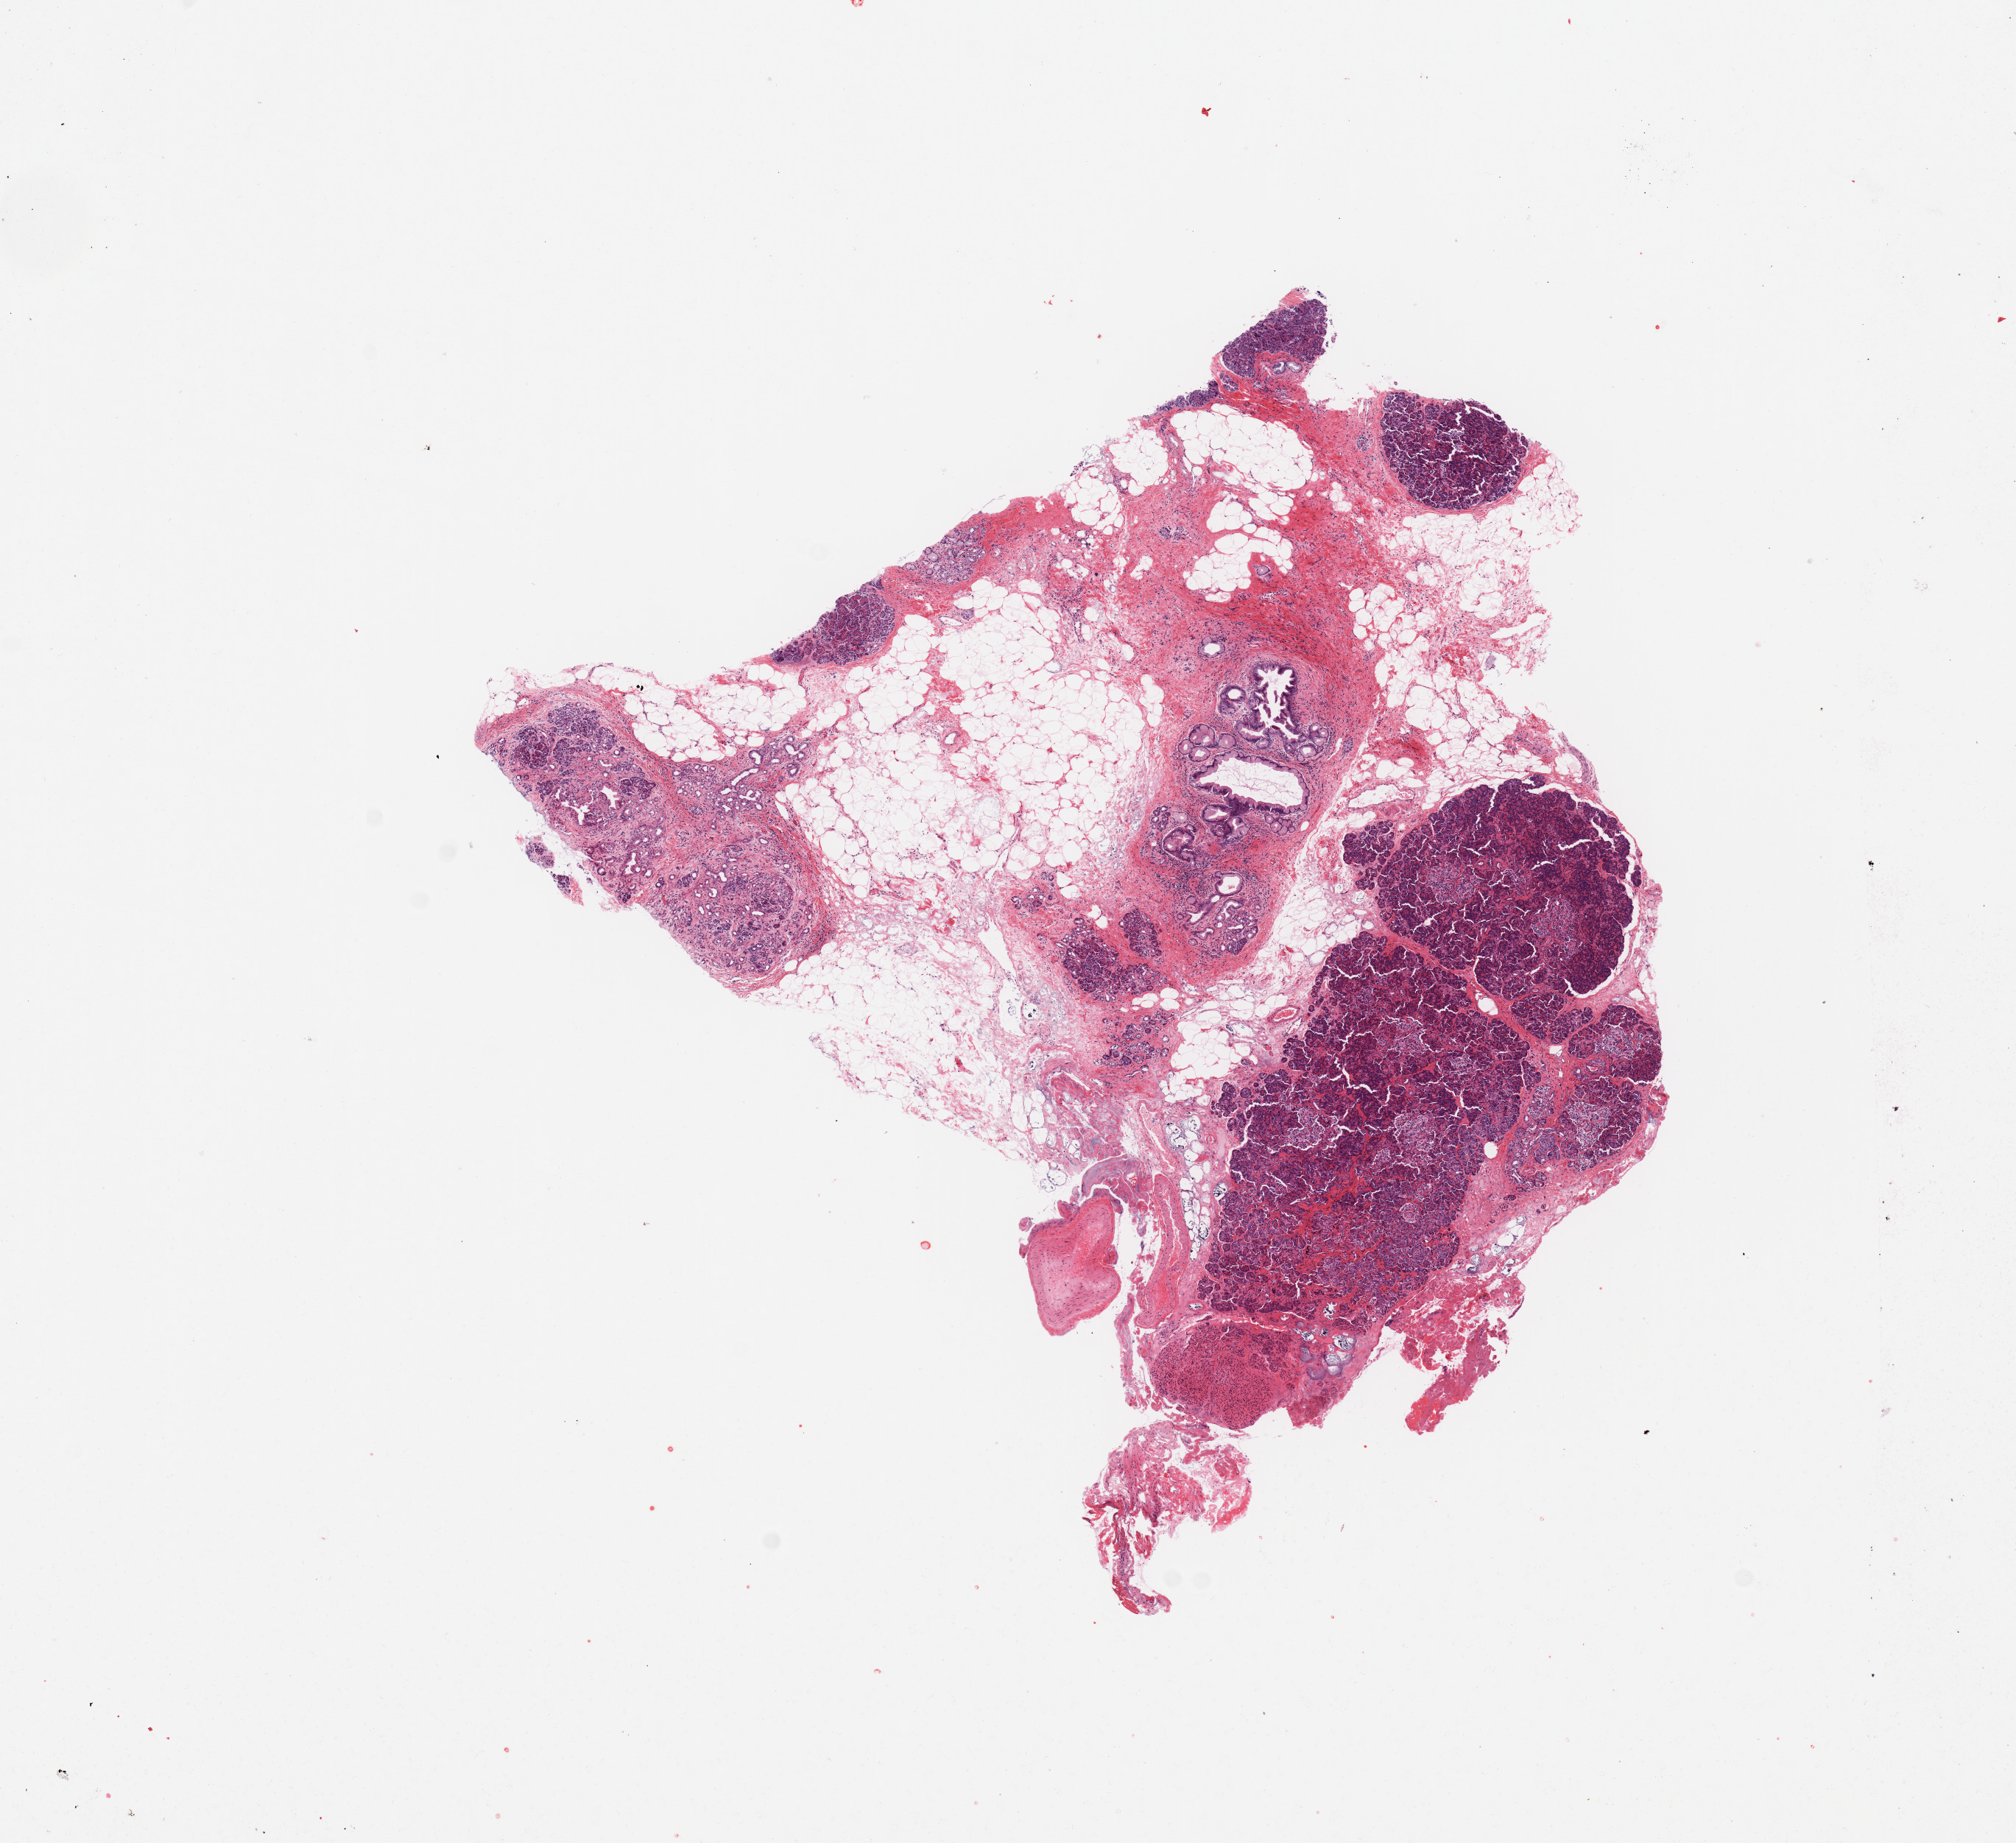
Whole-slide histology image, H&E-stained — whole scanned area (about 10.8 x 9.9 mm, acquisition: 20x scan) shown as a low-resolution overview, normal (non-tumour) tissue sample, sampled site: pancreas. Patient: male, age 43 years.
* this section: normal (non-tumour) tissue from the same patient
* patient diagnosis: Infiltrating duct carcinoma, NOS